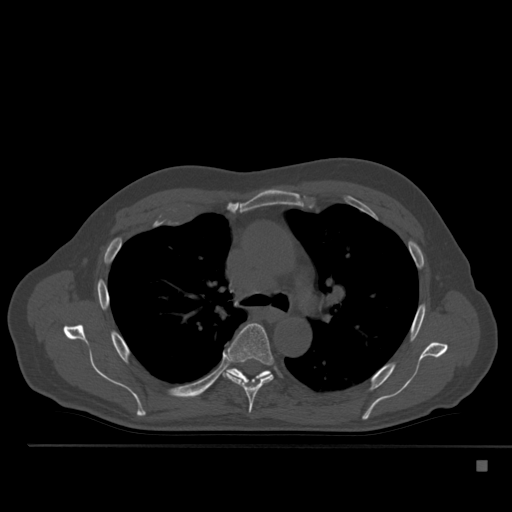
CT including the spine, one axial slice. Position 360 of 517 along the scan axis. Reconstruction kernel Br40s. 120 kVp. Bone window (W 1800 / L 400 HU). 1.5 mm slice thickness. 512 × 512 image matrix, field of view 408 × 408 mm. Patient: male, 70 years. From the clinical record (not read from this slice): primary cancer: renal.
Structures marked on this image (semi-automatically segmented with operator editing):
- T5 vertebra: box from (x=219, y=323) to (x=274, y=413) px
- T6 vertebra: (x=227, y=368)–(x=271, y=381)